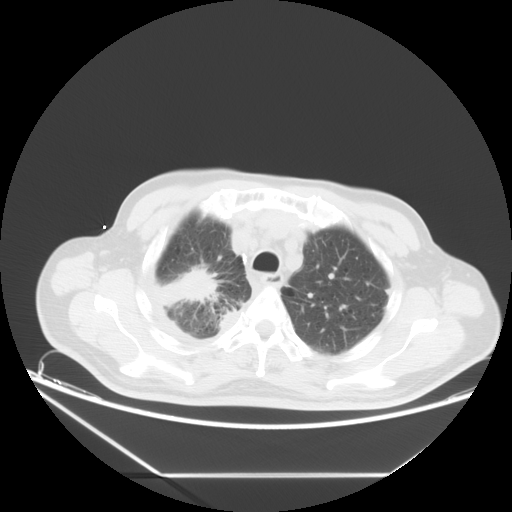
Chest CT, one axial slice. Position 14 of 20 along the scan axis. Reconstruction kernel STANDARD. 120 kVp. Lung window (W 1500 / L -600 HU). 5 mm slice thickness. 512 × 512 image matrix, field of view 418 × 418 mm. Patient: male, 75 years. From the clinical record (not read from this slice): clinical TNM (as recorded): T1c N1 M1.
Outlined on this slice (bounding box drawn by a radiologist):
- lung tumour (recorded histology: adenocarcinoma): bounding box <160,270,219,309> (left, top, right, bottom; pixels)